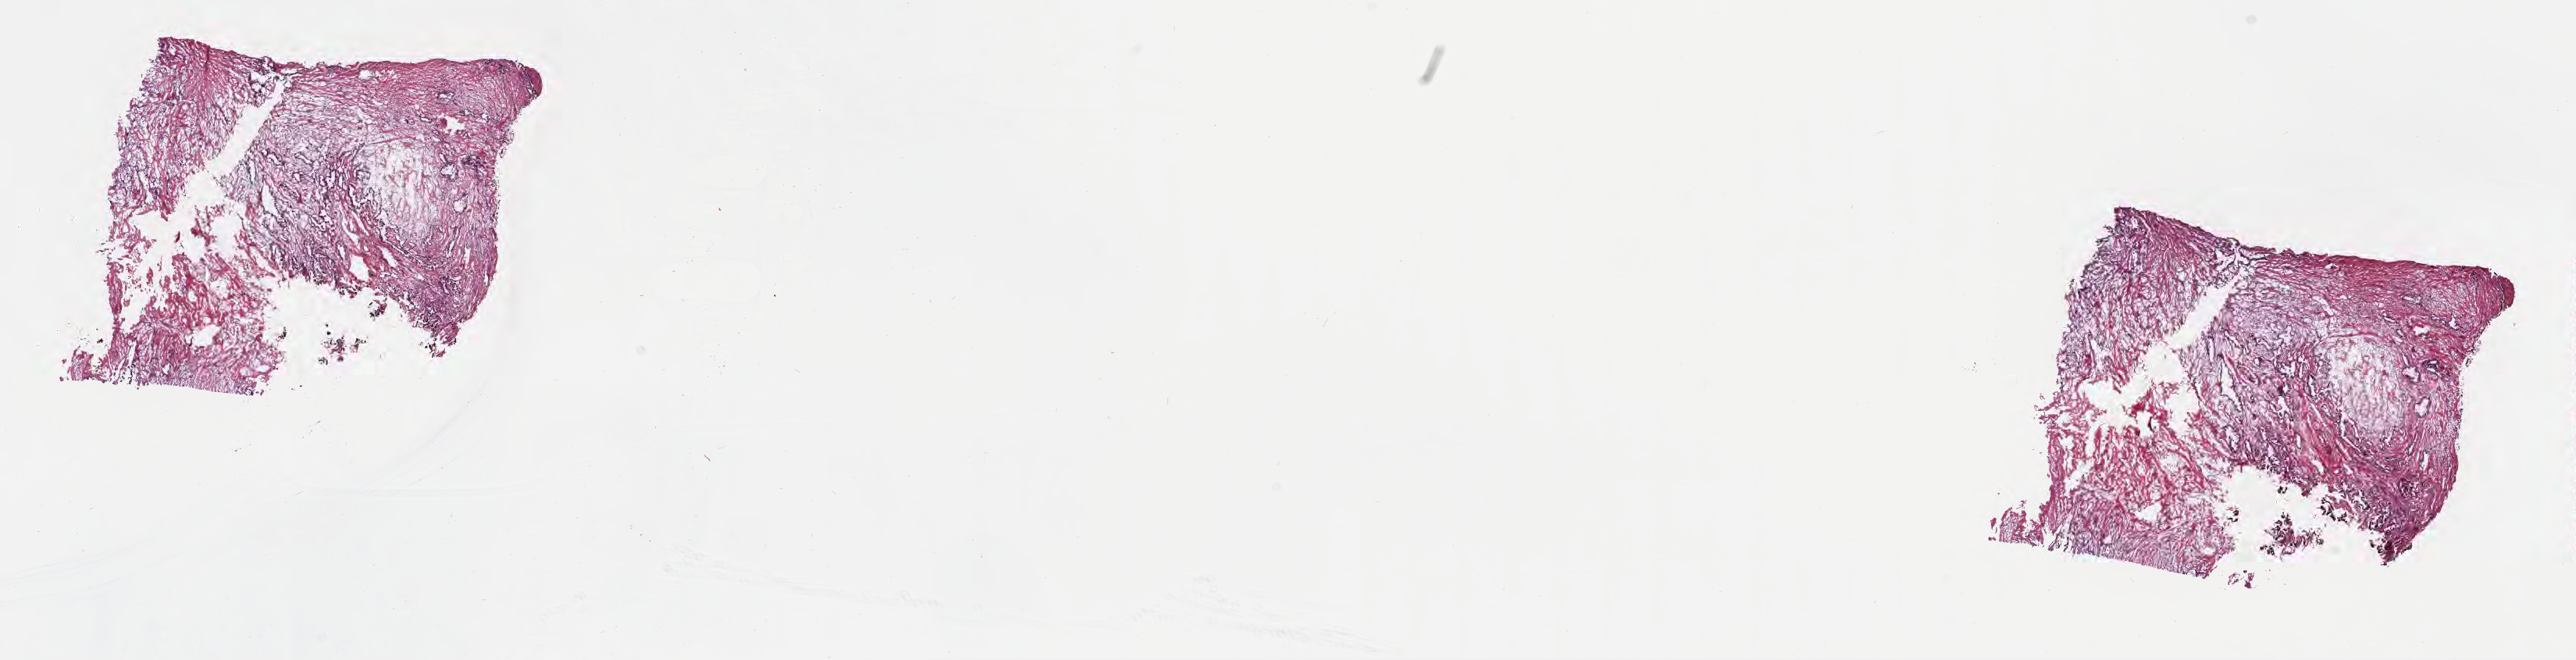
Hematoxylin and eosin (H&E) whole-slide image, whole scanned area (about 26.7 x 6.8 mm) shown as a low-resolution overview, frozen section (tissue freezing medium), primary tumor, anatomic site: body of pancreas. Male patient; age at initial diagnosis 79 years. Slide review estimates, as recorded: tumor cells 18%, tumor nuclei 70%, stromal cells 81%, necrosis 1%, normal cells 0%. Inflammatory infiltration, as recorded: lymphocyte infiltration 8%, monocyte infiltration 2%, neutrophil infiltration 0%.
Diagnosis: Infiltrating duct carcinoma, NOS. Section: top of the tissue portion.